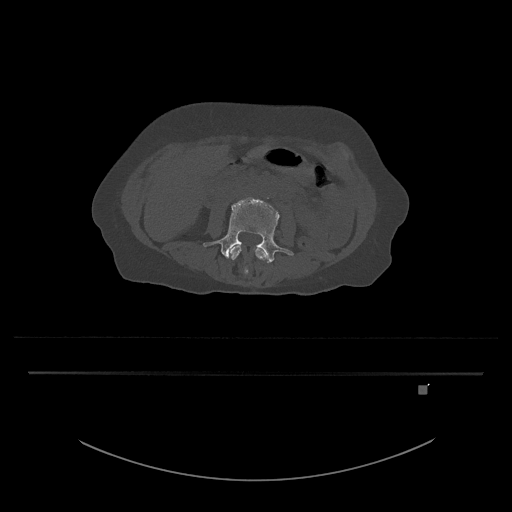
CT including the spine, one axial slice. Slice 382 of 797 in the series (ordered by position). Reconstruction kernel Br40s/3. 120 kVp. Bone window (W 1800 / L 400 HU). 0.5 mm slice thickness. 512 × 512 image matrix, field of view 500 × 500 mm. Female patient, age 57 years. Case-level facts recorded for this patient, not image findings: primary cancer: cervical.
Structures marked on this image (semi-automatic segmentation, software-assisted and operator-edited):
- L3 vertebra: bounding box [x1, y1, x2, y2] px = [230, 245, 267, 275]
- L4 vertebra: [203, 197, 294, 263]